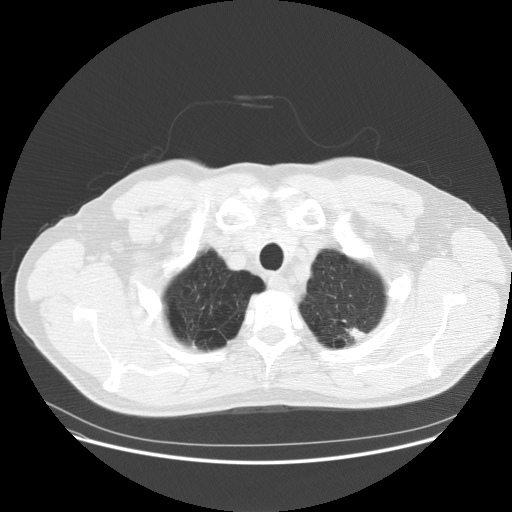
Low-dose screening chest CT, one axial slice; slice 148 of 158 in the series (ordered by position); reconstruction kernel STANDARD; lung window (W 1500 / L -600 HU); 512 × 512 image matrix, field of view 400 × 400 mm.
Annotated regions visible in this slice (expert manual segmentation):
- lesion 1 (tumor, upper lobe of left lung): box from (x=346, y=327) to (x=366, y=342) px